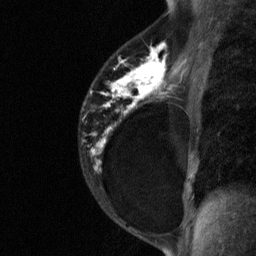
Breast MRI (dynamic contrast-enhanced), one sagittal slice. Dynamic contrast-enhanced study with each time point stored as its own series, time point 2 of 3 at this slice position (early post-contrast, ordered by acquisition time). 1.5 T. TE 4.8 ms, TR 27 ms. 2 mm slice thickness. 256 × 256 image matrix, field of view 180 × 180 mm. Female patient, age 34 years. From the clinical record (not read from this slice): setting: breast cancer imaged before/during neoadjuvant chemotherapy; receptor status: HR-positive, HER2-negative.
Outlined on this slice (semi-automatic segmentation, software-assisted and operator-edited):
- analysis volume of interest (the breast-tissue region the enhancement analysis was run in; not a lesion): bounding box (x1, y1, x2, y2) in pixels: (79, 44, 181, 191)
- tumour enhancement mask (voxels above the 90 % enhancement threshold inside the analysis volume of interest): (91, 44, 167, 171)